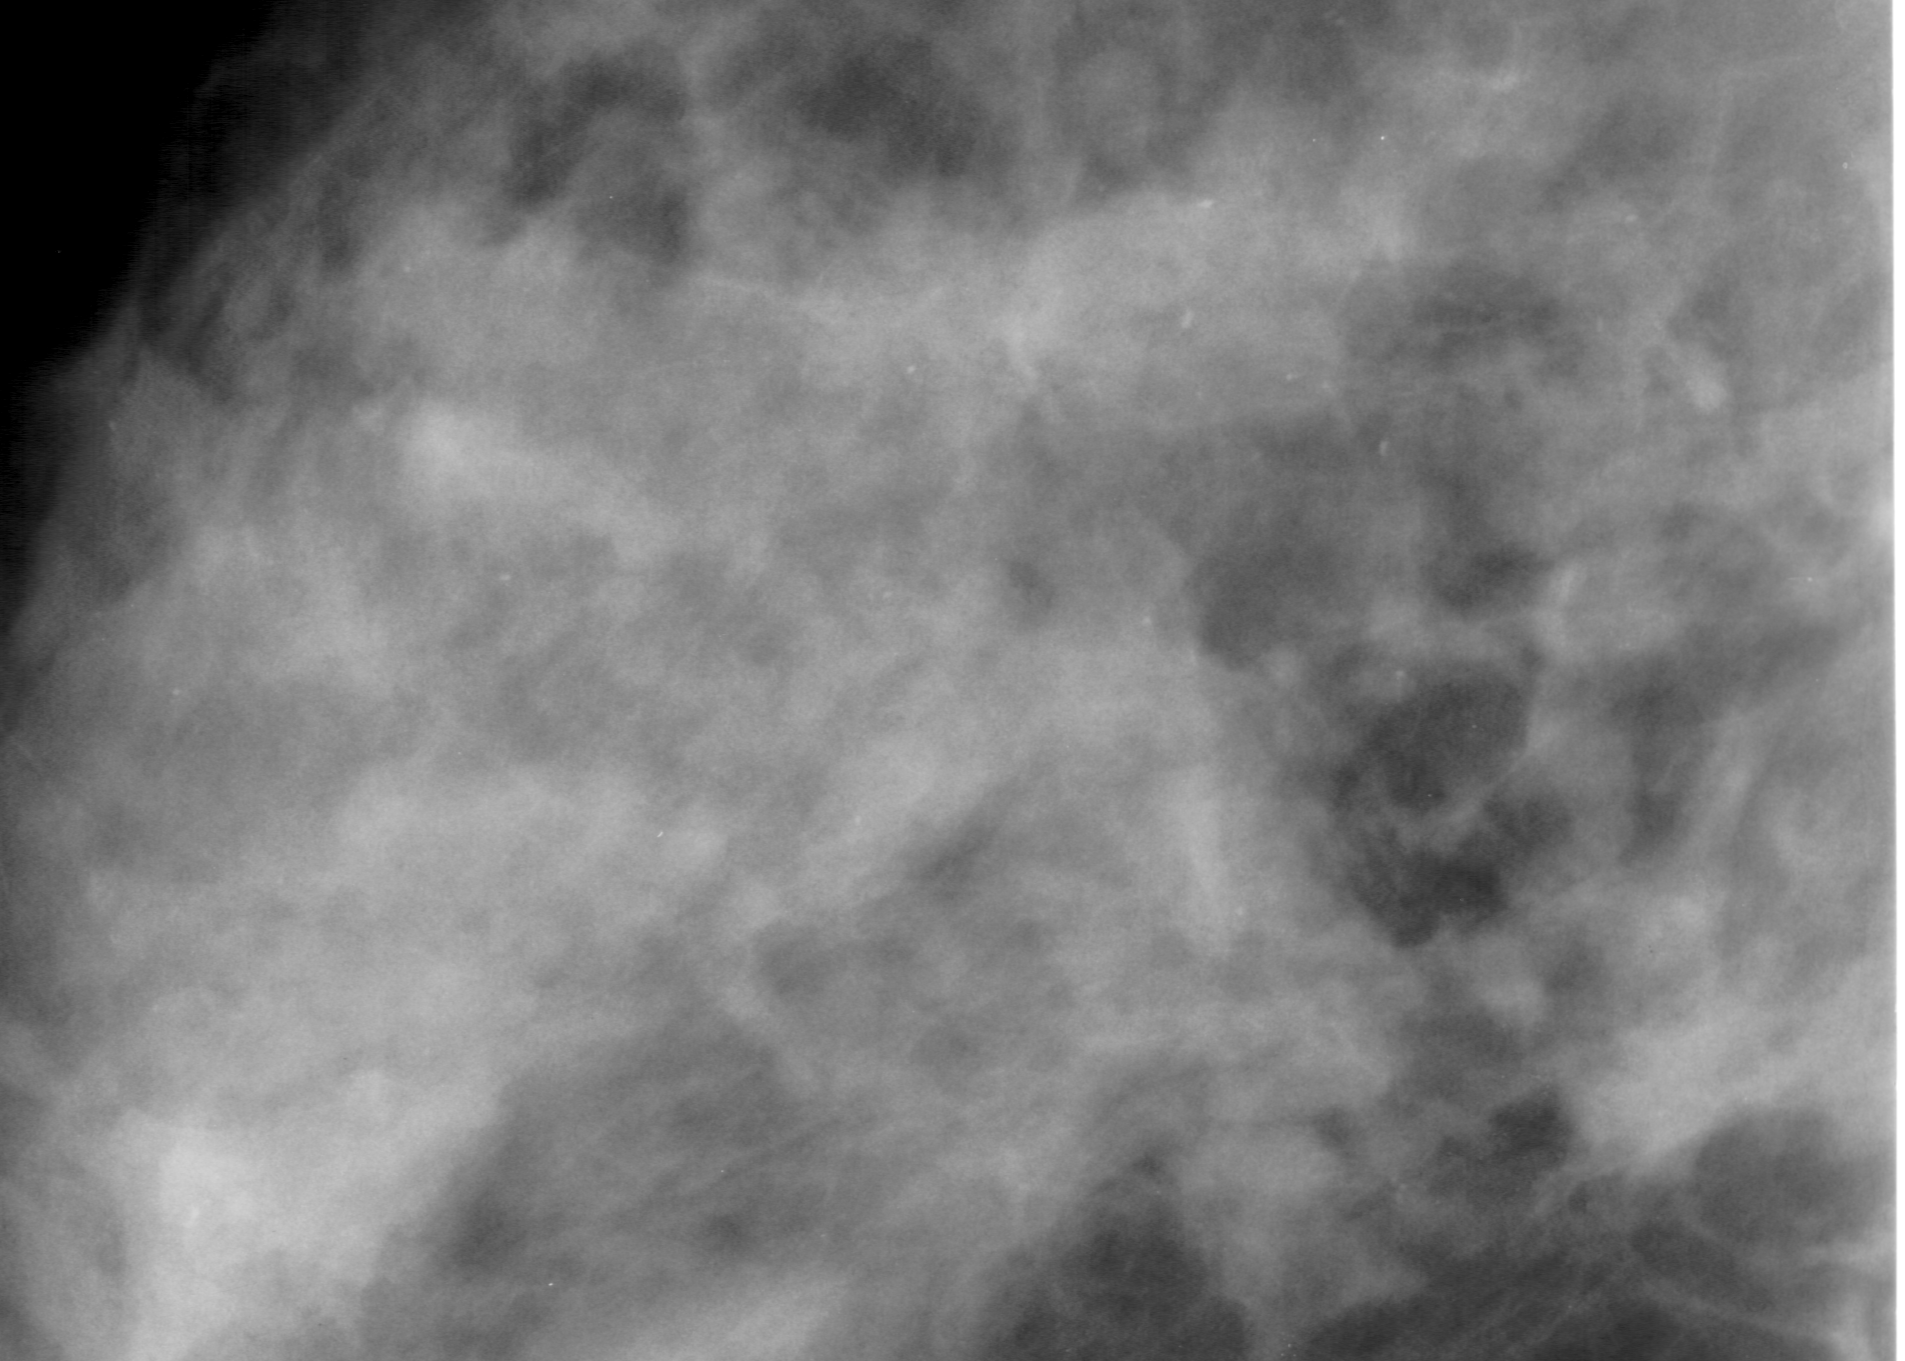
Cropped region of a digitized screen-film mammogram centred on a radiologist-marked abnormality, left breast, MLO view.
Finding: calcifications, morphology pleomorphic, distribution segmental; BI-RADS assessment category 4; pathology (as recorded): malignant.